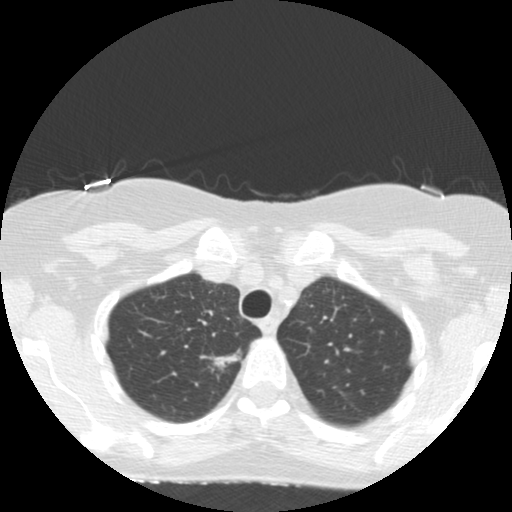
Low-dose screening chest CT, axial slice; first (baseline) screen; lung window (W 1500 / L -600 HU). Female, age 67 years at enrolment. Former smoker at enrolment.
- Lesion marked by an expert reader, bounding box (x1, y1, x2, y2) in pixels: (195, 339, 254, 387).
- Reader record for this screening exam (exam-level; its link to the box is not recorded): non-calcified nodule or mass ≥4 mm, right upper lobe, 16 × 7 mm, poorly defined margins, mixed attenuation.
- Official screen result: positive, change unspecified: nodule(s) >= 4 mm or enlarging nodule(s), mass(es), or other non-specific abnormalities suspicious for lung cancer.
- Later outcome: lung cancer diagnosed 132 days after this screen — adenocarcinoma, NOS, right upper lobe, moderately differentiated (G2), stage IA (AJCC 6th edition), 13 mm at pathology.